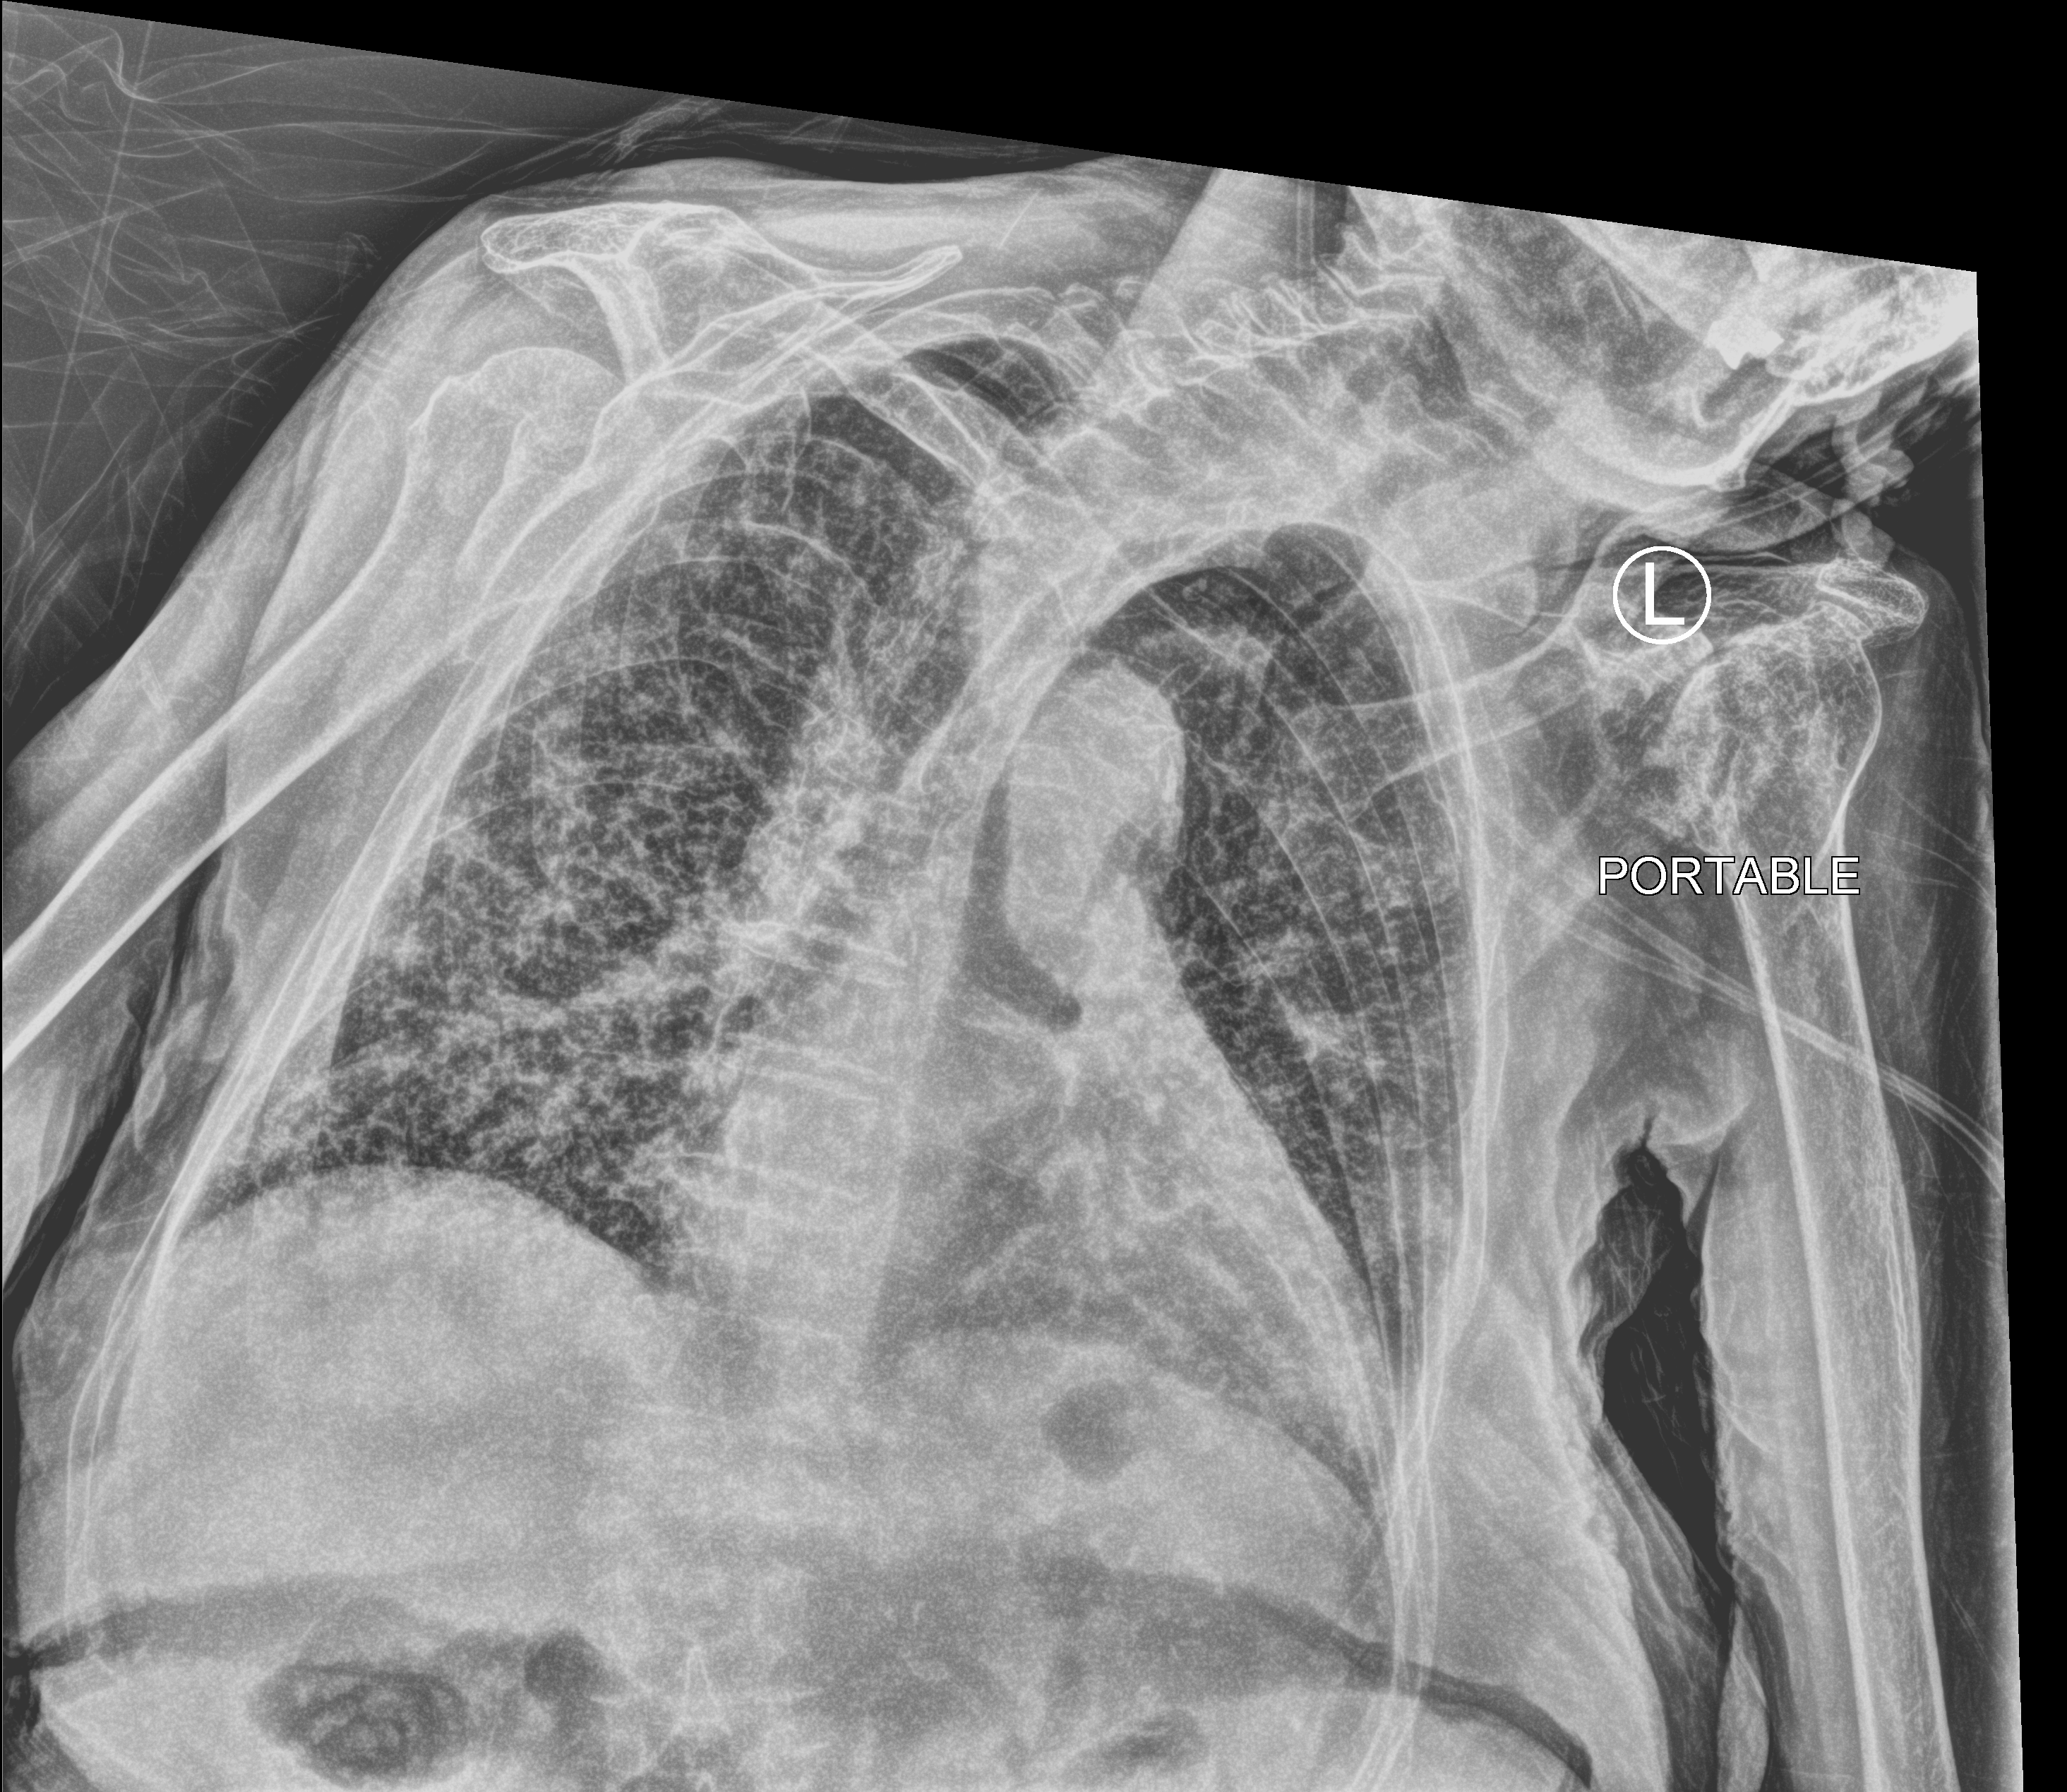
Portable chest radiograph, anteroposterior (AP) projection. Patient hospitalised with COVID-19; female, aged 75–90 years.
From the hospital-stay record, not from the radiograph (when in the stay this image was taken is not recorded): mechanically ventilated during this hospital stay: no.